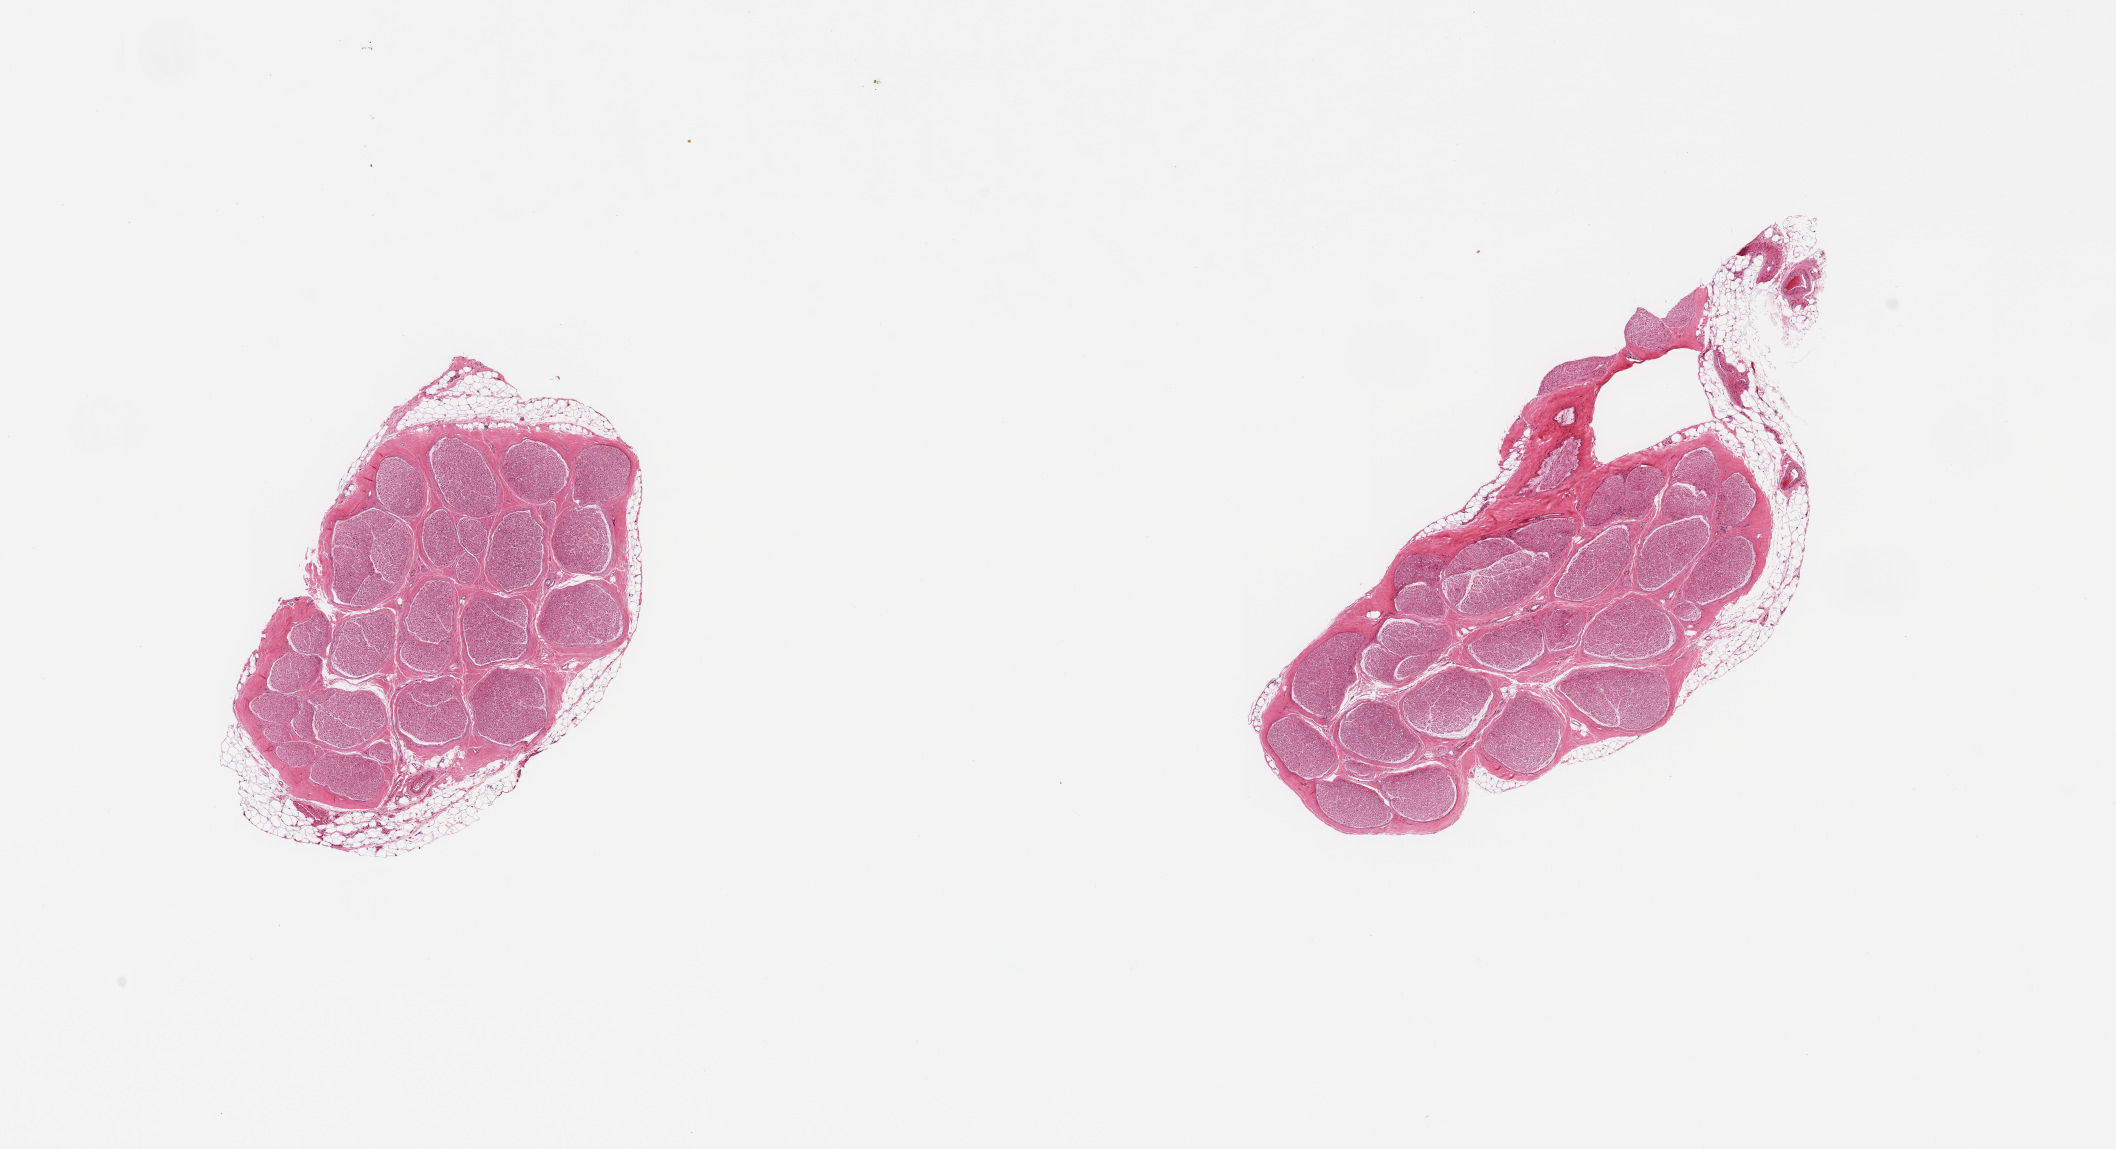
Hematoxylin and eosin (H&E) whole-slide image, brightfield, a low-resolution overview of the entire scanned area, about 16.7 x 9.1 mm; PAXgene-fixed, paraffin-embedded tissue; sampled site (target tissue): tibial nerve; donor tissue sample. Donor: male.
Reviewer comment on this tissue sample: 2 pieces, few nubbins of adherent fat up to ~0.5mm.